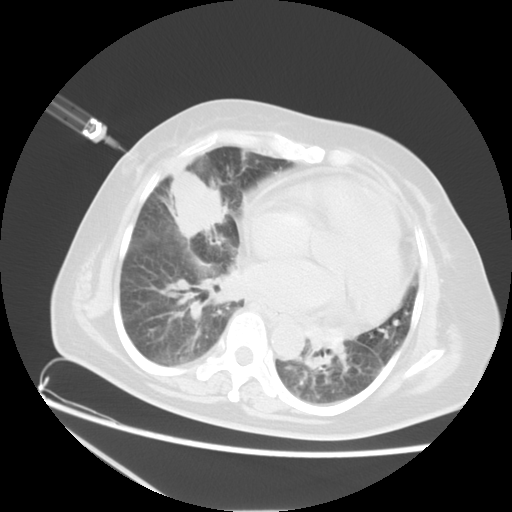
Chest CT, one axial slice; slice 8 of 21 in the series (ordered by position); 120 kVp; lung window (W 1500 / L -600 HU); 5 mm slice thickness; 512 × 512 image matrix. Female patient, age 67 years. From the clinical record (not read from this slice): clinical TNM (as recorded): T2a N3 M1a.
Structures marked on this image (rectangle marked by the reading radiologist):
- lung tumour (recorded histology: adenocarcinoma): bounding box [x1, y1, x2, y2] px = [170, 172, 228, 239]